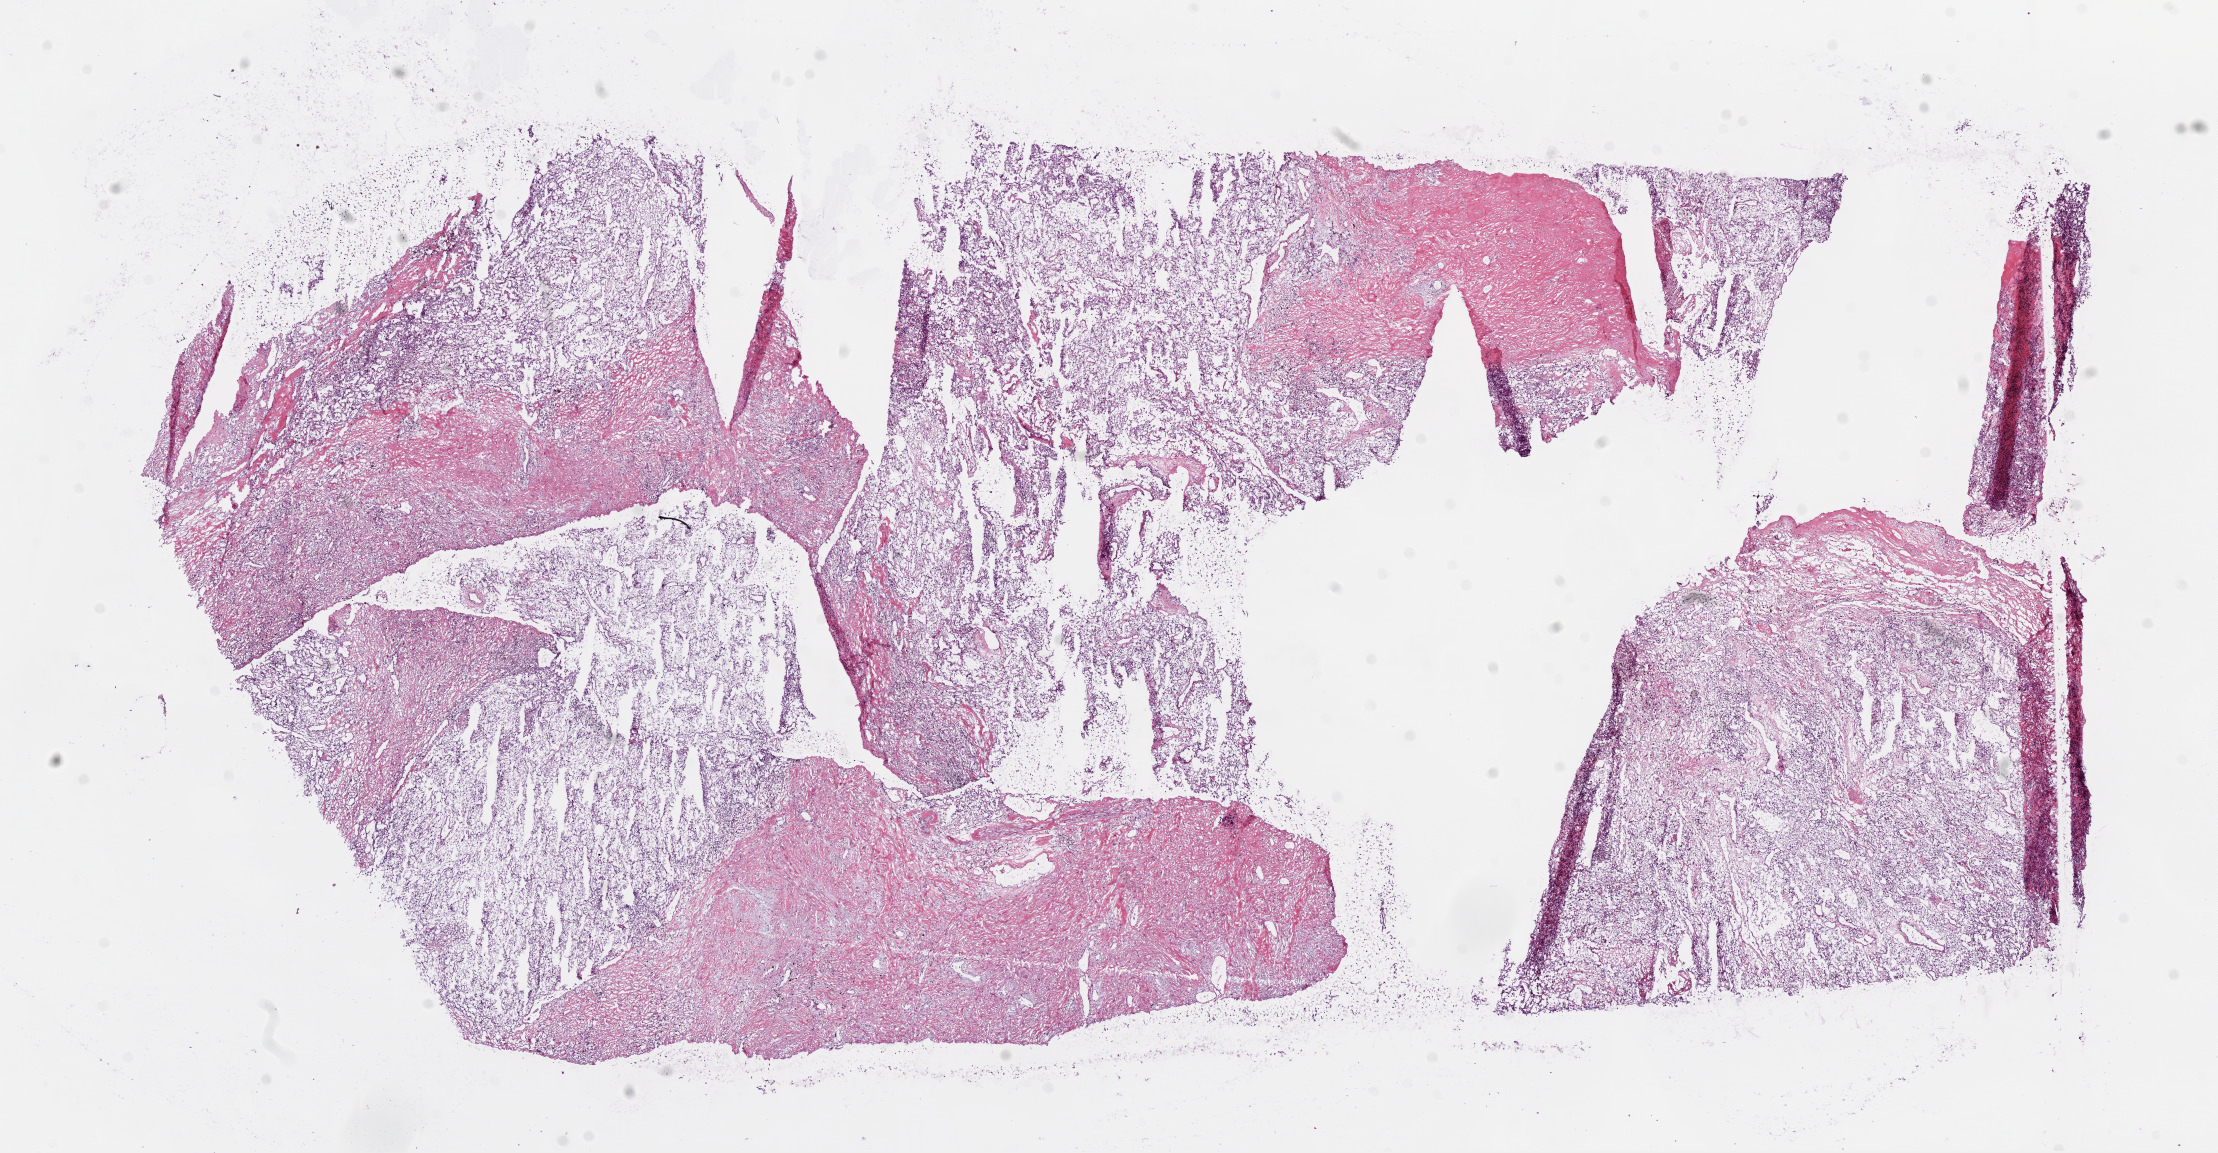
Digitized H&E tissue section (whole slide) — whole scanned area (about 17.9 x 9.3 mm) shown as a low-resolution overview. Frozen section from the top of the tissue portion. Kidney, primary tumour sample. Patient: male, age at initial diagnosis 51 years. Slide review estimates, as recorded: tumour cells 60%, tumour nuclei 75%.
Diagnosis: Clear cell adenocarcinoma, NOS.